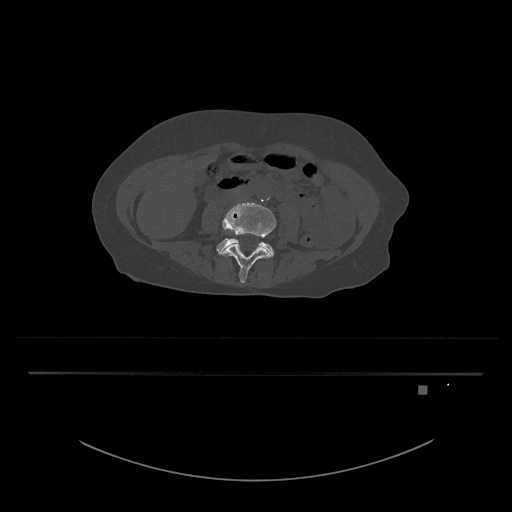
CT including the spine, one axial slice; slice 344 of 797 in the series (ordered by position); reconstruction kernel Br40s/3; 120 kVp; bone window (W 1800 / L 400 HU); 512 × 512 image matrix, field of view 500 × 500 mm. Patient: female, 57 years. From the clinical record (not read from this slice): primary cancer: cervical.
Outlined on this slice (semi-automatic segmentation, software-assisted and operator-edited):
- L4 vertebra: box from (x=220, y=202) to (x=277, y=283) px